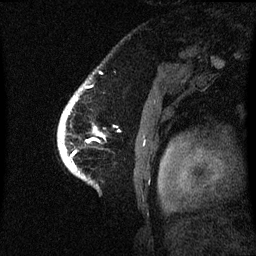
Breast MRI (dynamic contrast-enhanced), one sagittal slice; position 52 of 60 along the scan axis; dynamic contrast-enhanced series, image 2 of 3 at this slice position (ordered by acquisition); 1.5 T; TE 4.2 ms, TR 8.4 ms; 256 × 256 image matrix, field of view 220 × 220 mm. Female patient, age 53 years. Case-level facts recorded for this patient, not image findings: setting: breast cancer imaged before/during neoadjuvant chemotherapy; receptor status: HR-positive, HER2-negative.
Outlined on this slice (semi-automatic segmentation, software-assisted and operator-edited):
- analysis volume of interest (the breast-tissue region the enhancement analysis was run in; not a lesion): bounding box (x1, y1, x2, y2) in pixels: (59, 96, 104, 171)
- tumour enhancement mask (voxels above the 70 % enhancement threshold inside the analysis volume of interest): (61, 112, 69, 147)